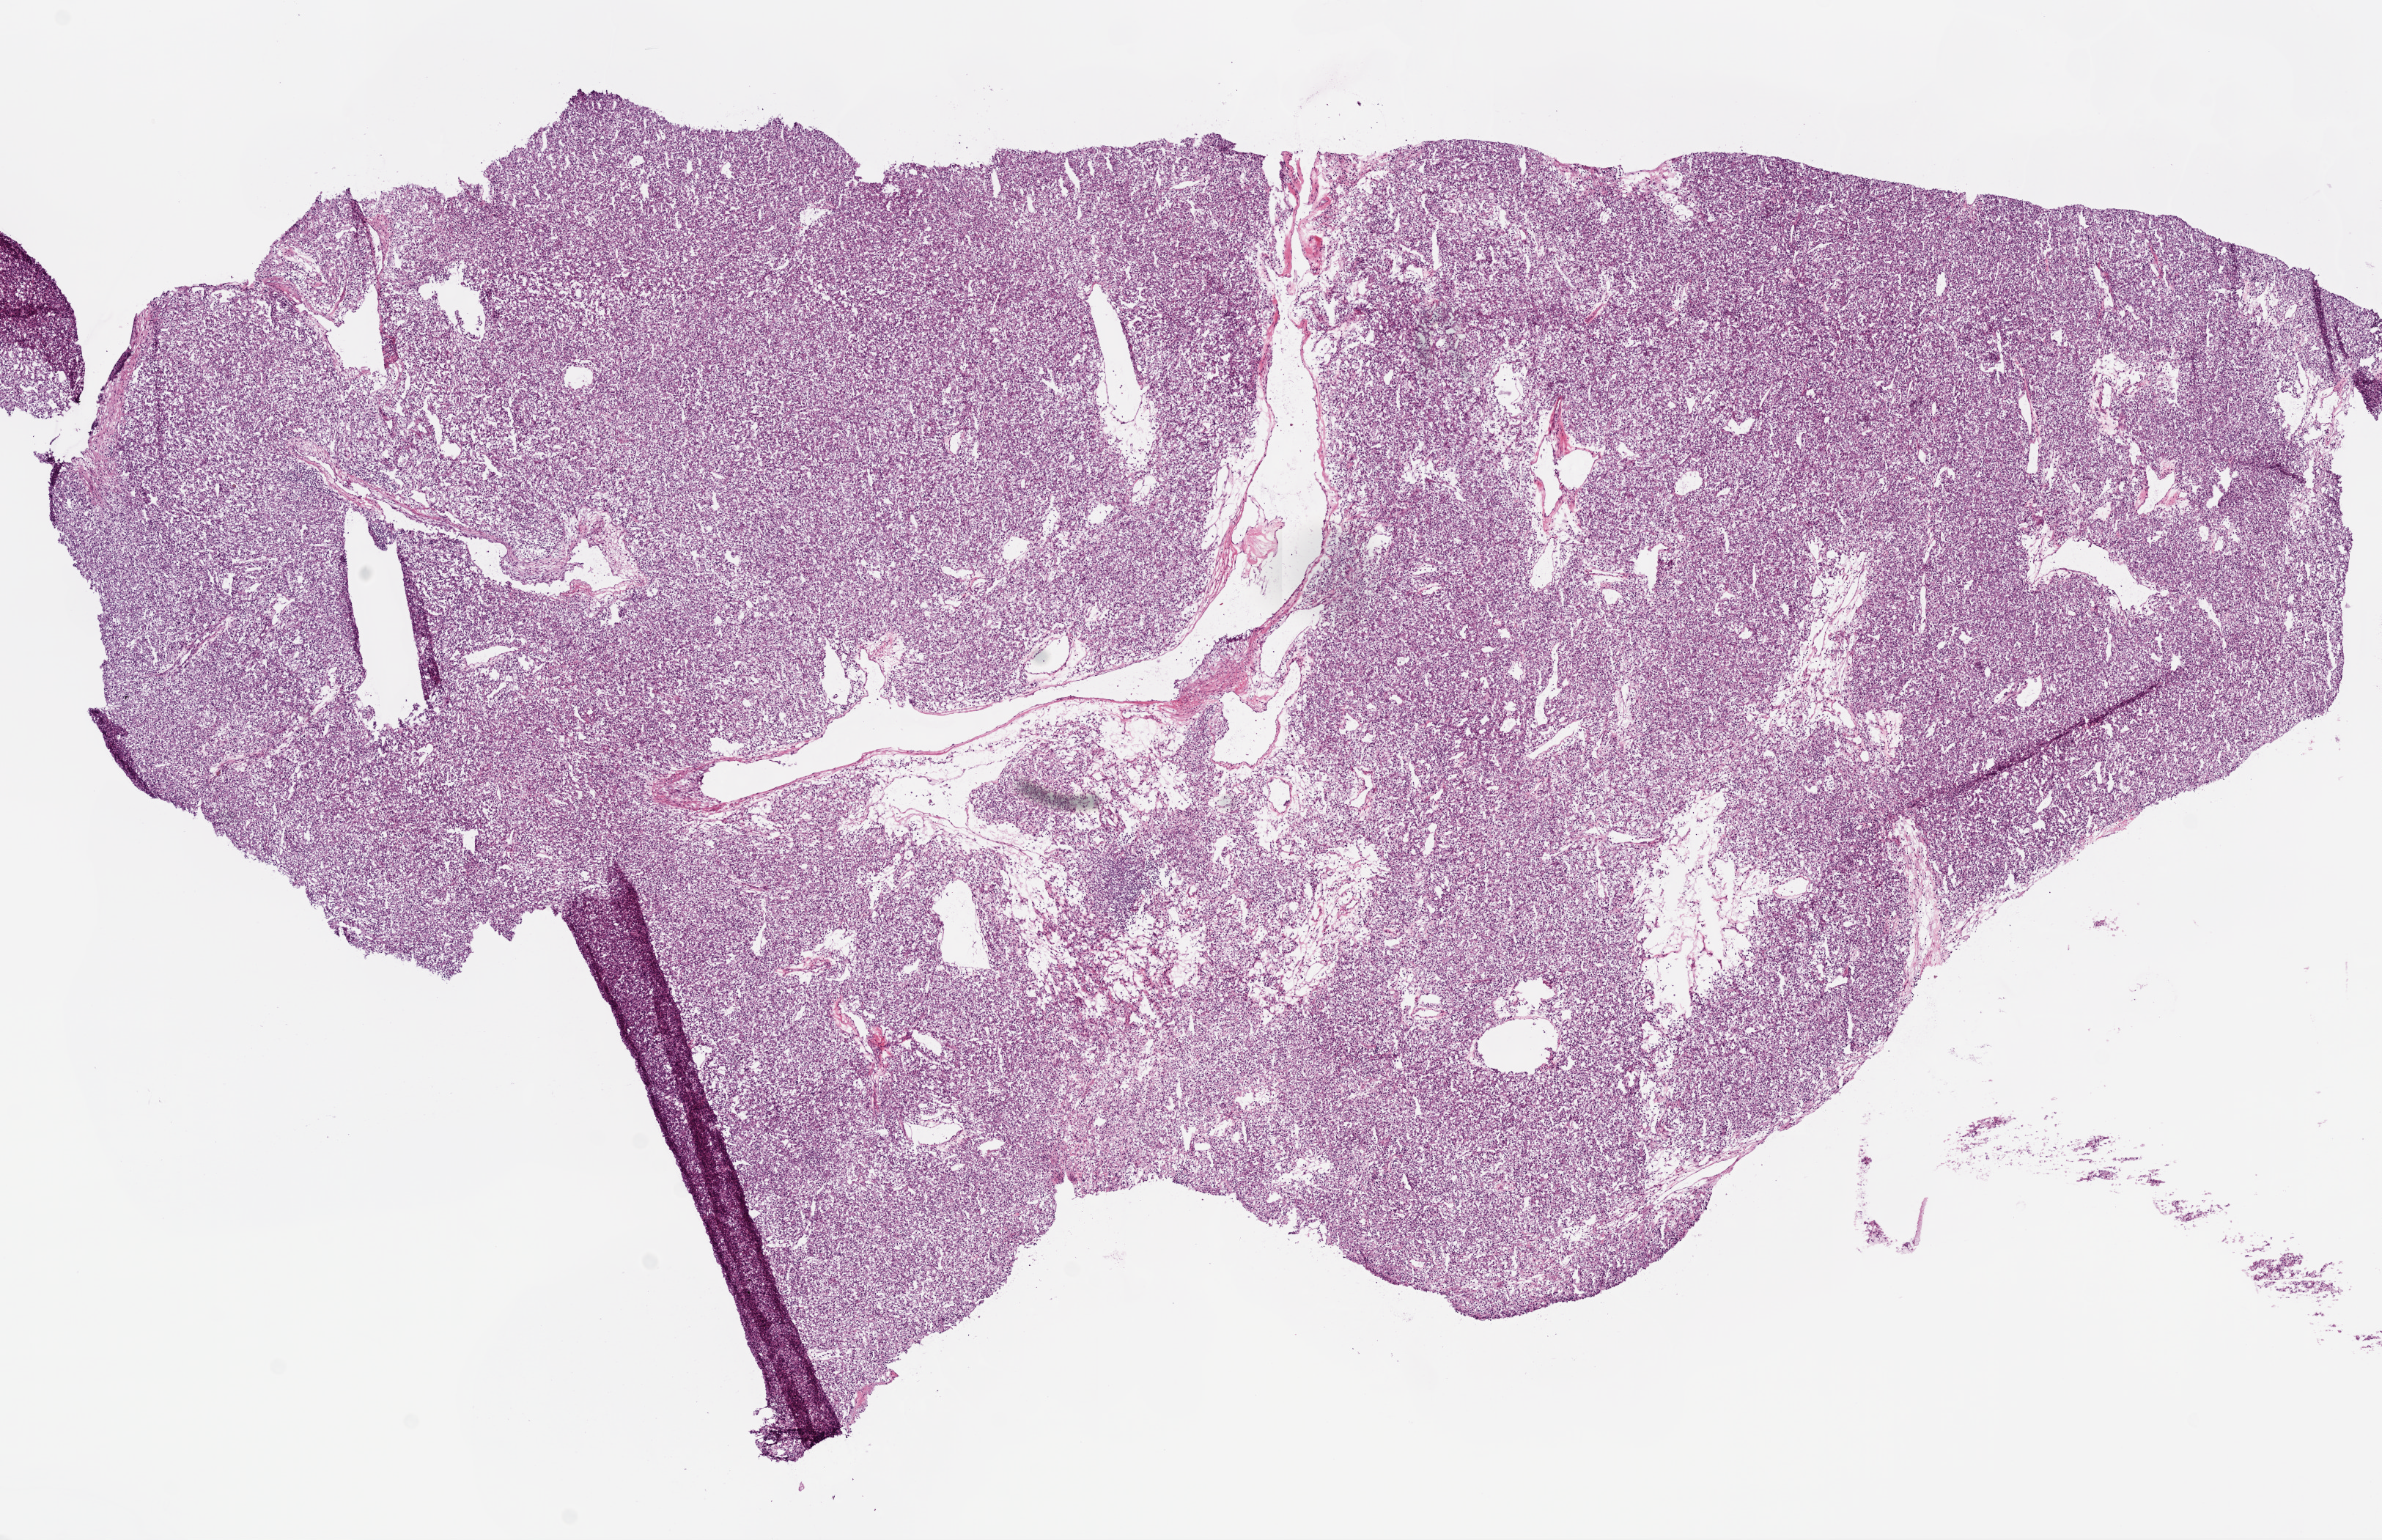
Whole-slide histology image, Hematoxylin and eosin (H&E) stained, low-resolution overview of the scanned area, about 13.0 x 8.4 mm, frozen section from the top of the tissue portion, primary tumour sample from the kidney. Female, age 65 years at initial diagnosis. Histologic grade: G2 (moderately differentiated). Pathologist review of this section (percent, as recorded): tumour cells 90%, tumour nuclei 85%, normal cells 0%, stromal cells 8%, necrosis 0%.
TNM: T1 N0 M0. AJCC pathologic stage: I (5th edition). Pathologic diagnosis: Clear cell adenocarcinoma, NOS. Laterality: left.